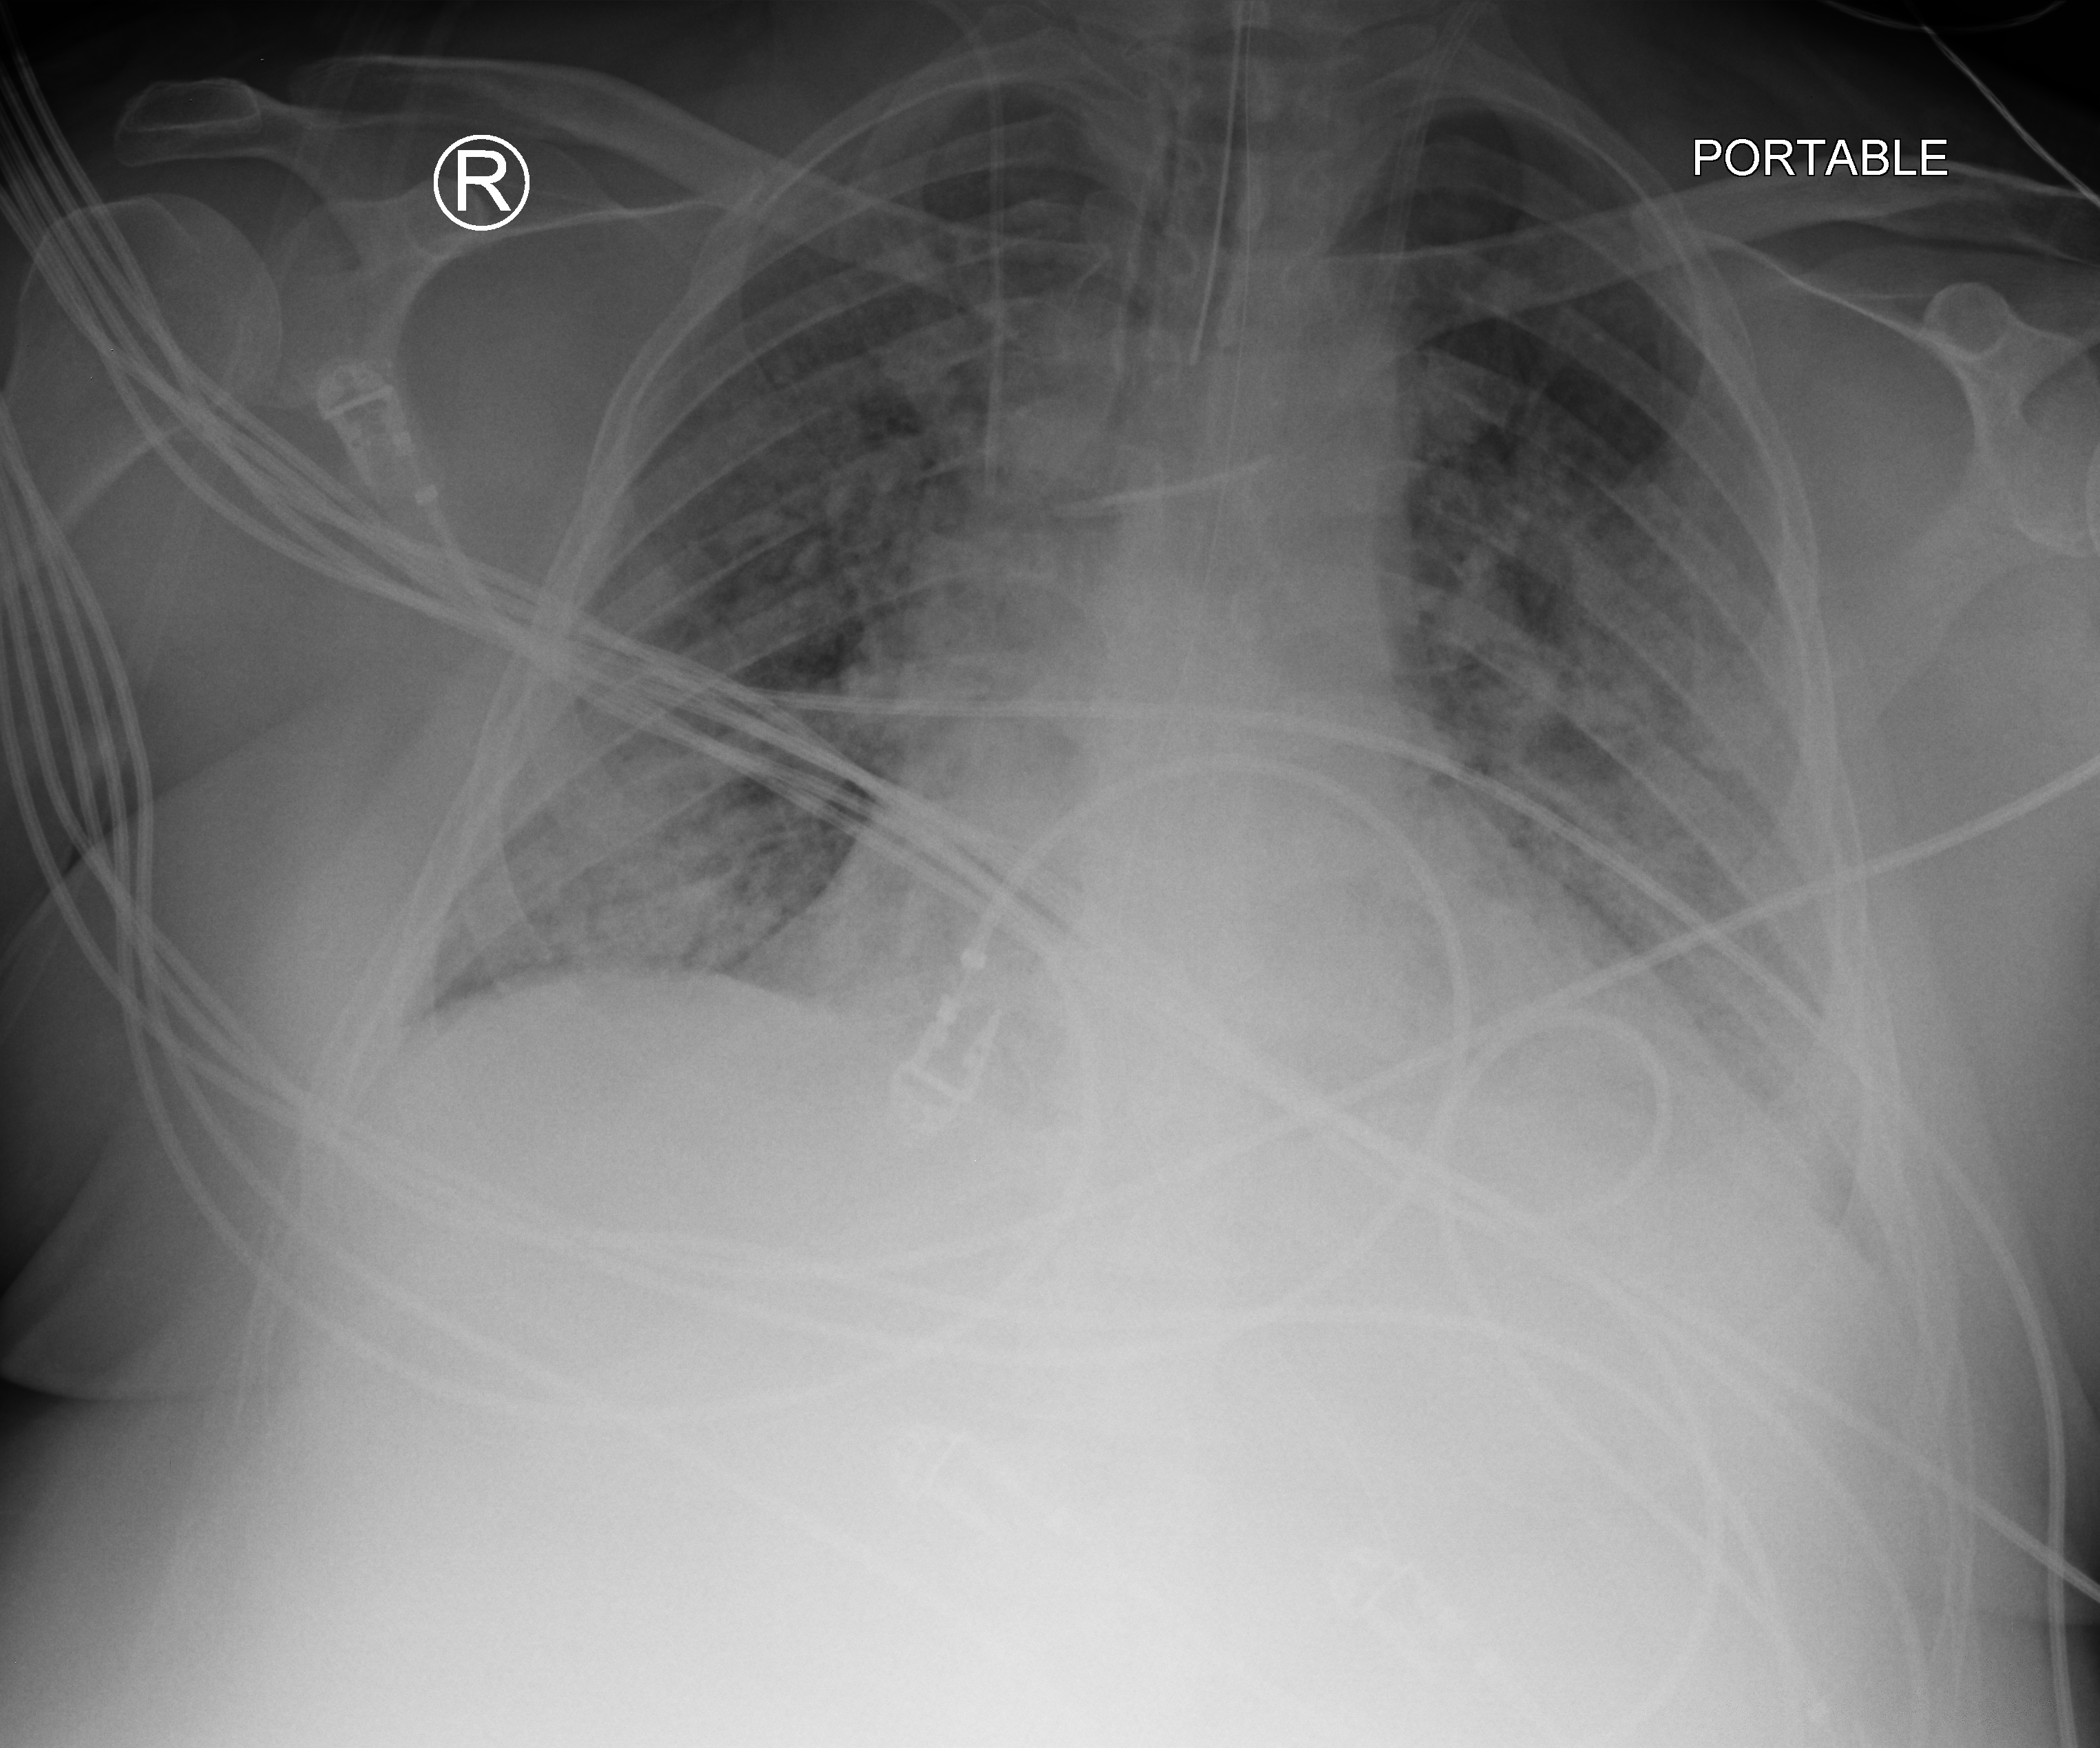
Portable chest radiograph; anteroposterior (AP) projection. Patient hospitalised with COVID-19; male, aged 18–59 years.
From the hospital-stay record, not from the radiograph (when in the stay this image was taken is not recorded): length of hospital stay: 39 days; admitted to intensive care during this hospital stay: yes.